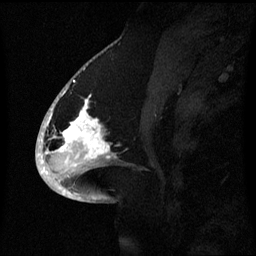
Breast MRI (dynamic contrast-enhanced), one sagittal slice; position 31 of 60 along the scan axis; dynamic contrast-enhanced series, image 2 of 3 at this slice position (ordered by acquisition); 1.5 T; TE 4.2 ms, TR 8.4 ms; 2.1 mm slice thickness; 256 × 256 image matrix, field of view 220 × 220 mm. Female patient, age 53 years. From the clinical record (not read from this slice): setting: breast cancer imaged before/during neoadjuvant chemotherapy; receptor status: HR-positive, HER2-negative.
Annotated regions visible in this slice (semi-automatically segmented with operator editing):
- analysis volume of interest (the breast-tissue region the enhancement analysis was run in; not a lesion): bounding box (x1, y1, x2, y2) in pixels: (52, 90, 121, 171)
- tumour enhancement mask (voxels above the 70 % enhancement threshold inside the analysis volume of interest): (52, 90, 111, 159)